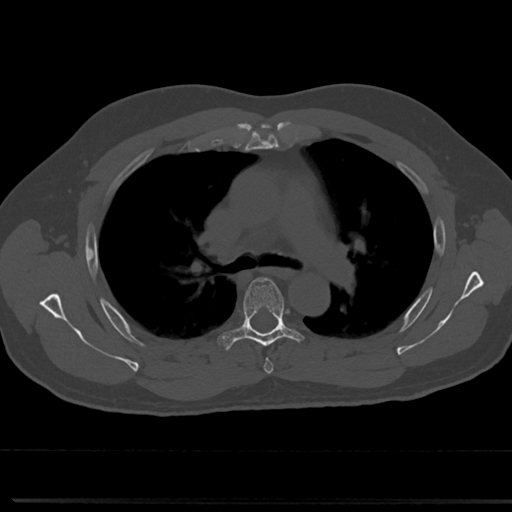
CT including the spine, one axial slice; reconstruction kernel Br40s/3; 120 kVp; bone window (W 1800 / L 400 HU); 0.5 mm slice thickness; 512 × 512 image matrix, field of view 355 × 355 mm. Patient: male, 61 years. Case-level facts recorded for this patient, not image findings: primary cancer: prostate.
Outlined on this slice (semi-automatically segmented with operator editing):
- T4 vertebra: bounding box [x1, y1, x2, y2] px = [262, 345, 273, 374]
- T5 vertebra: [218, 276, 310, 352]